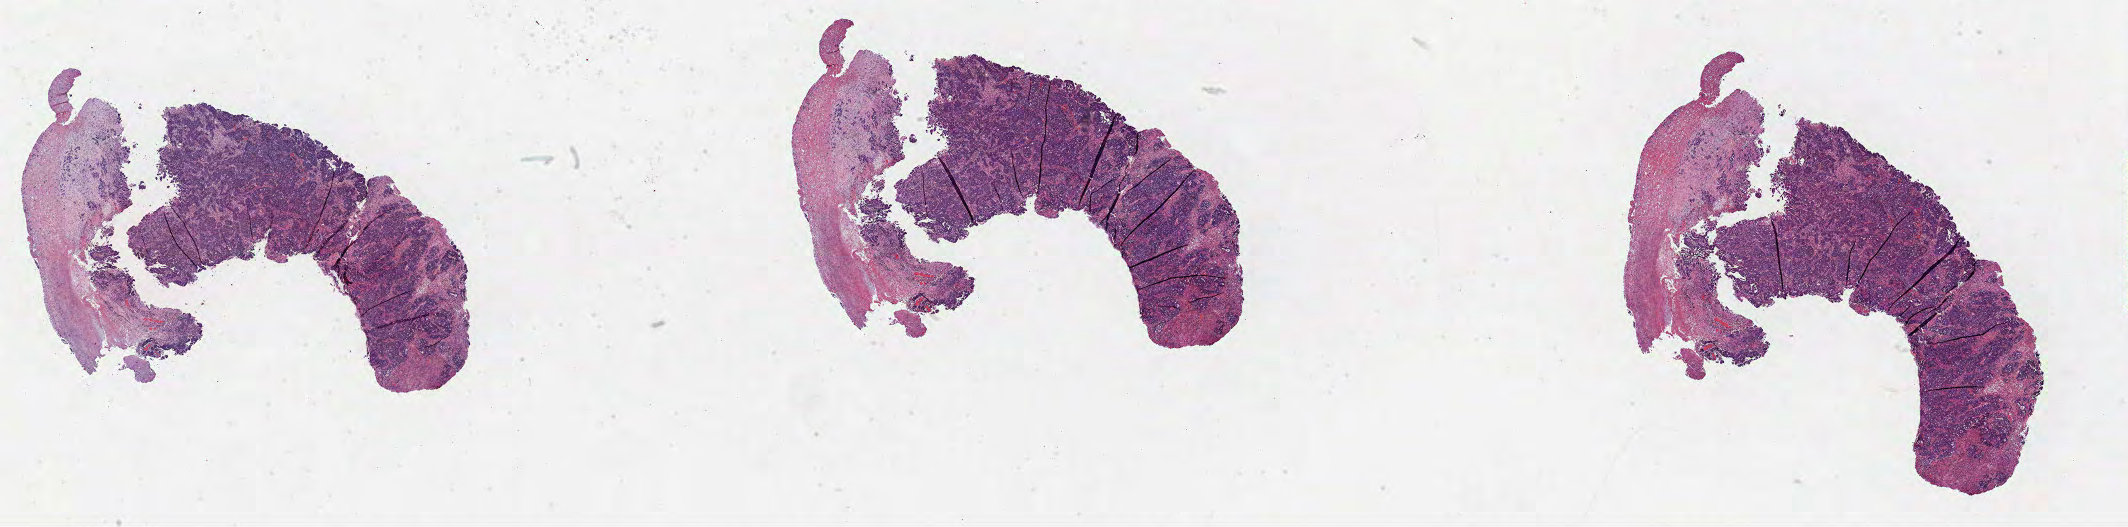
Whole-slide histology image, H&E, a low-resolution overview of the entire scanned area, about 34.3 x 8.5 mm. FFPE section. Ovary, primary tumour sample. Female patient; age at initial diagnosis 49 years.
Diagnosis: Serous cystadenocarcinoma, NOS.